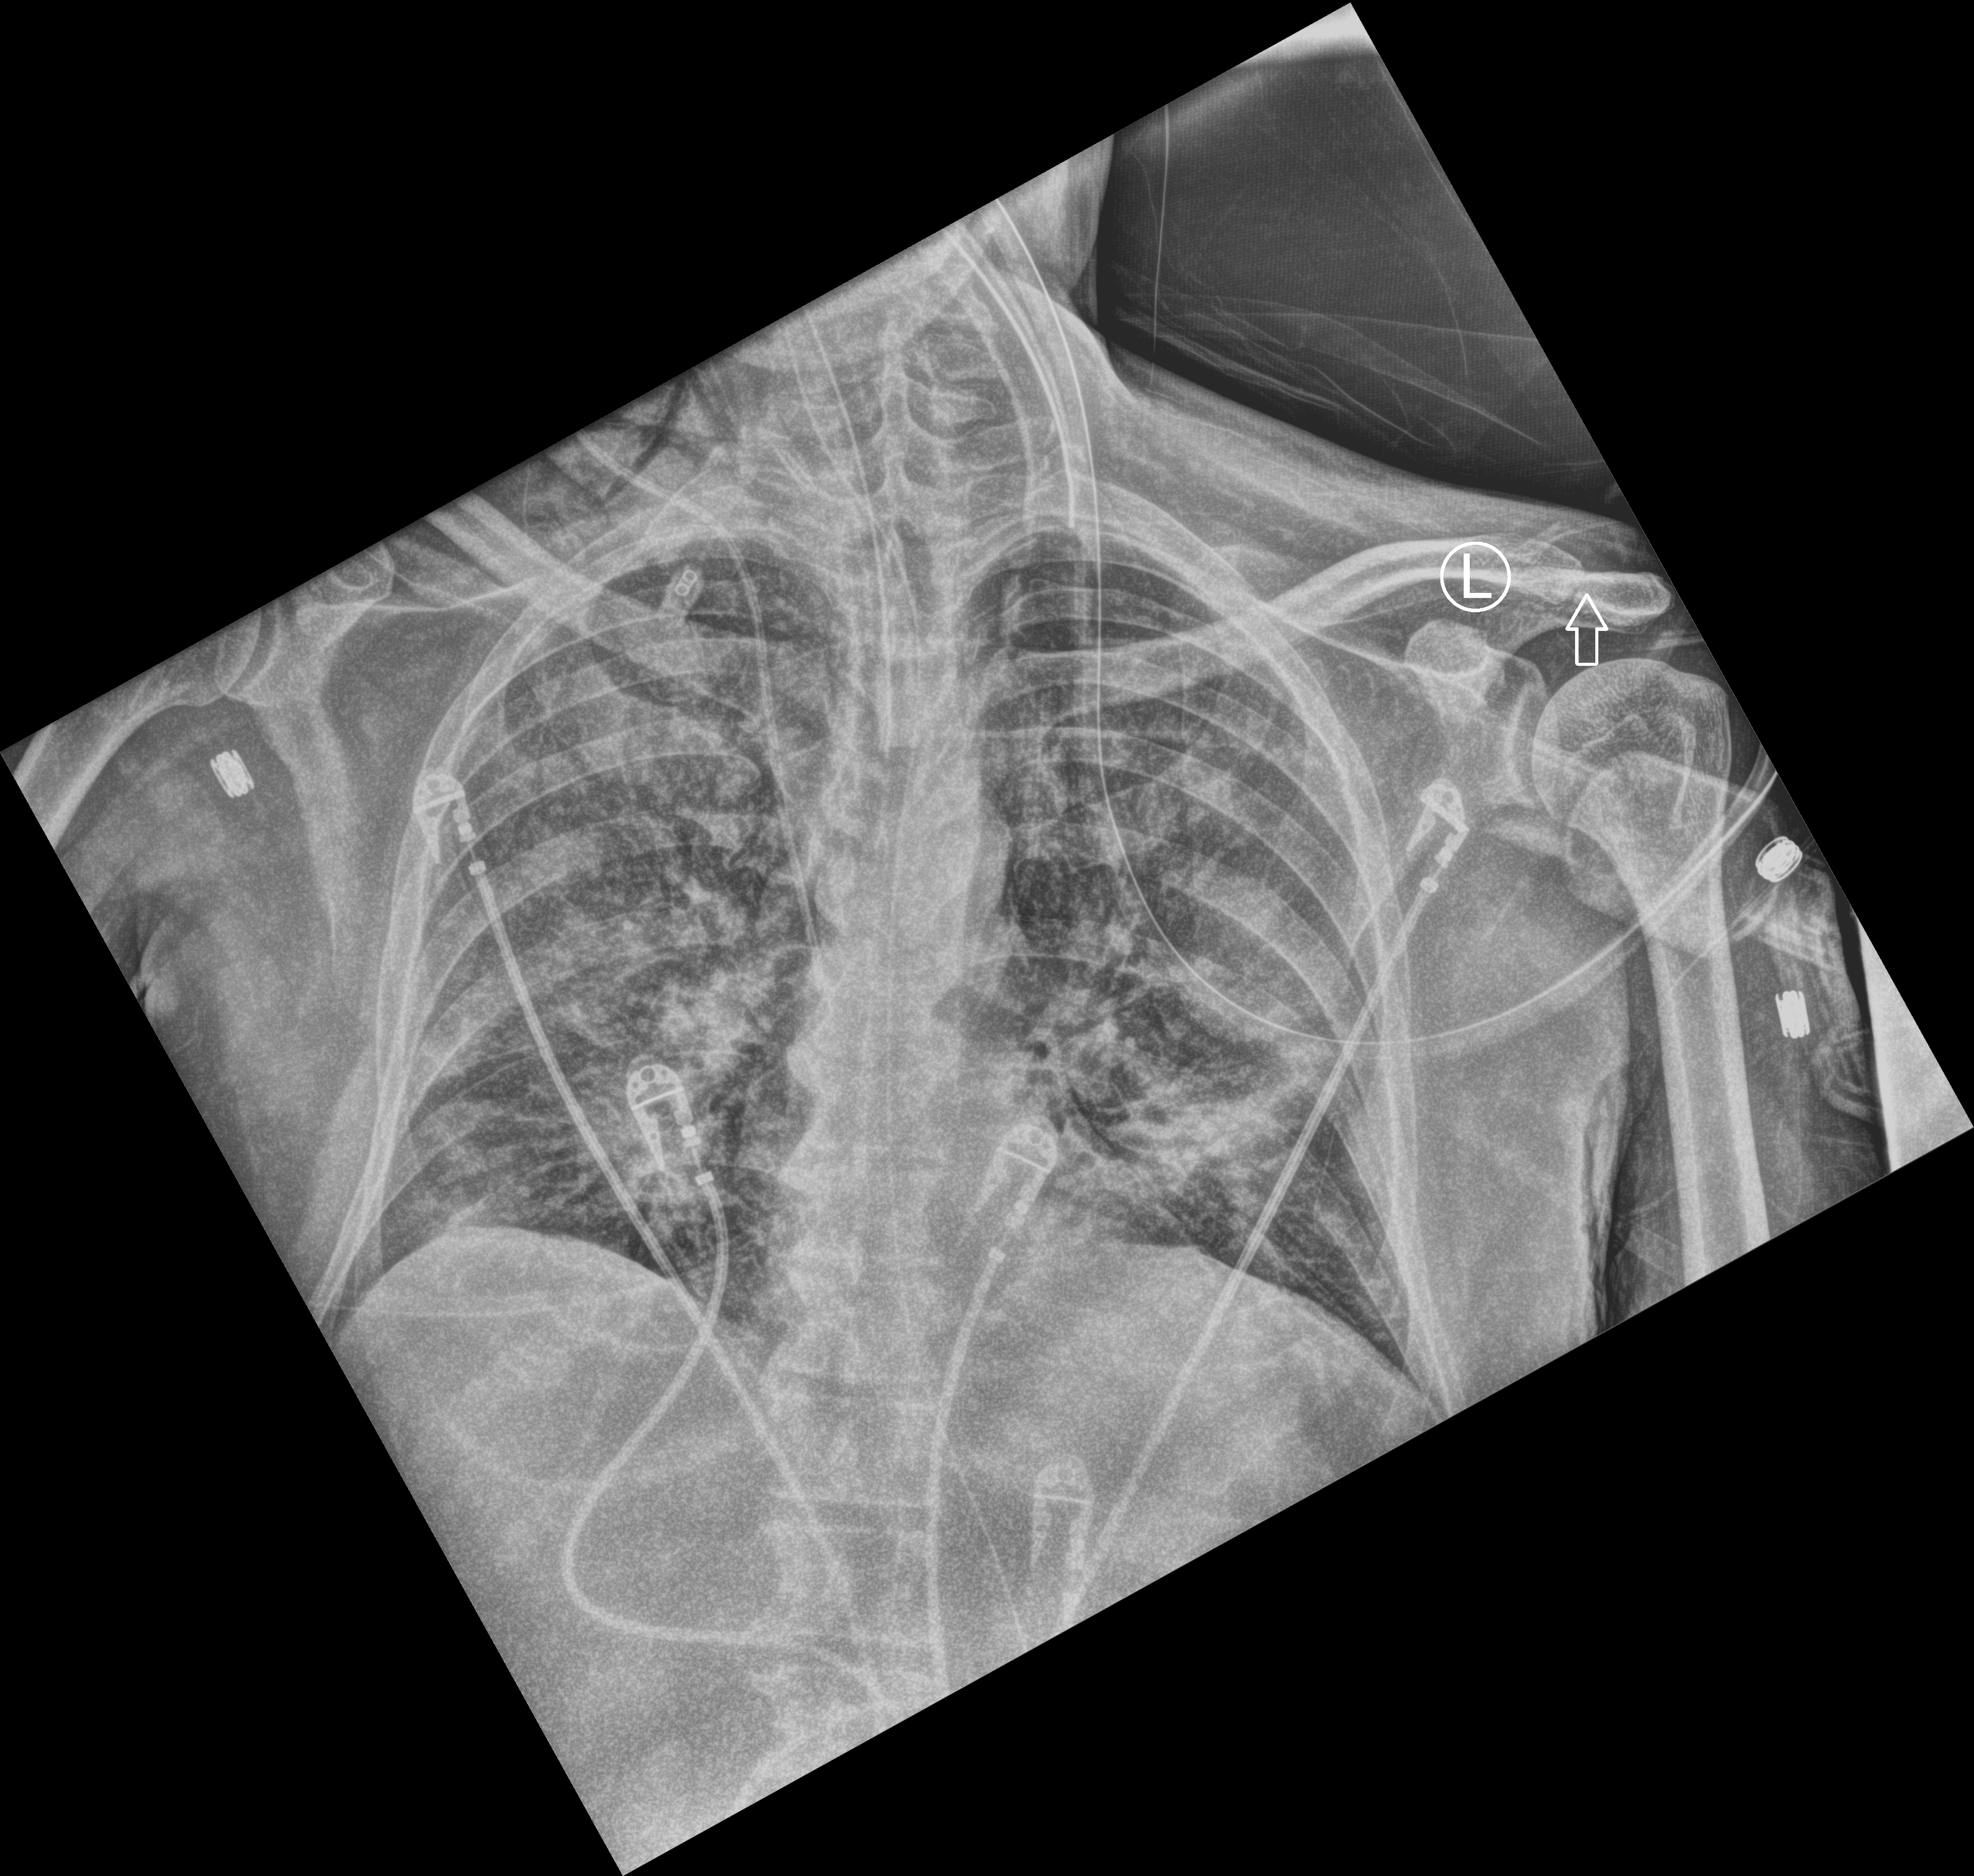
Portable chest radiograph. Male patient hospitalised with COVID-19, age 60–74 years.
Hospital-stay facts (about this admission, not read from this image; timing relative to this image not recorded): admitted to intensive care during this hospital stay: yes; mechanically ventilated during this hospital stay: yes.